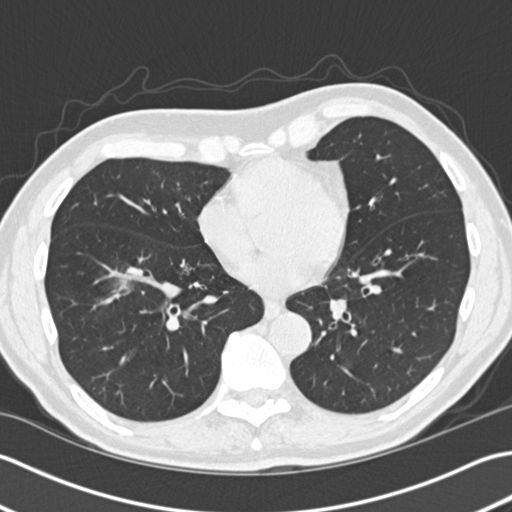
Low-dose screening chest CT, one axial slice; position 67 of 172 along the scan axis; 120 kVp; lung window (W 1500 / L -600 HU); 2 mm slice thickness; 512 × 512 image matrix, field of view 350 × 350 mm.
Structures marked on this image (outlined manually by an expert reader):
- lesion 1 (tumor, lower lobe of right lung): bounding box <111,266,143,297> (left, top, right, bottom; pixels)